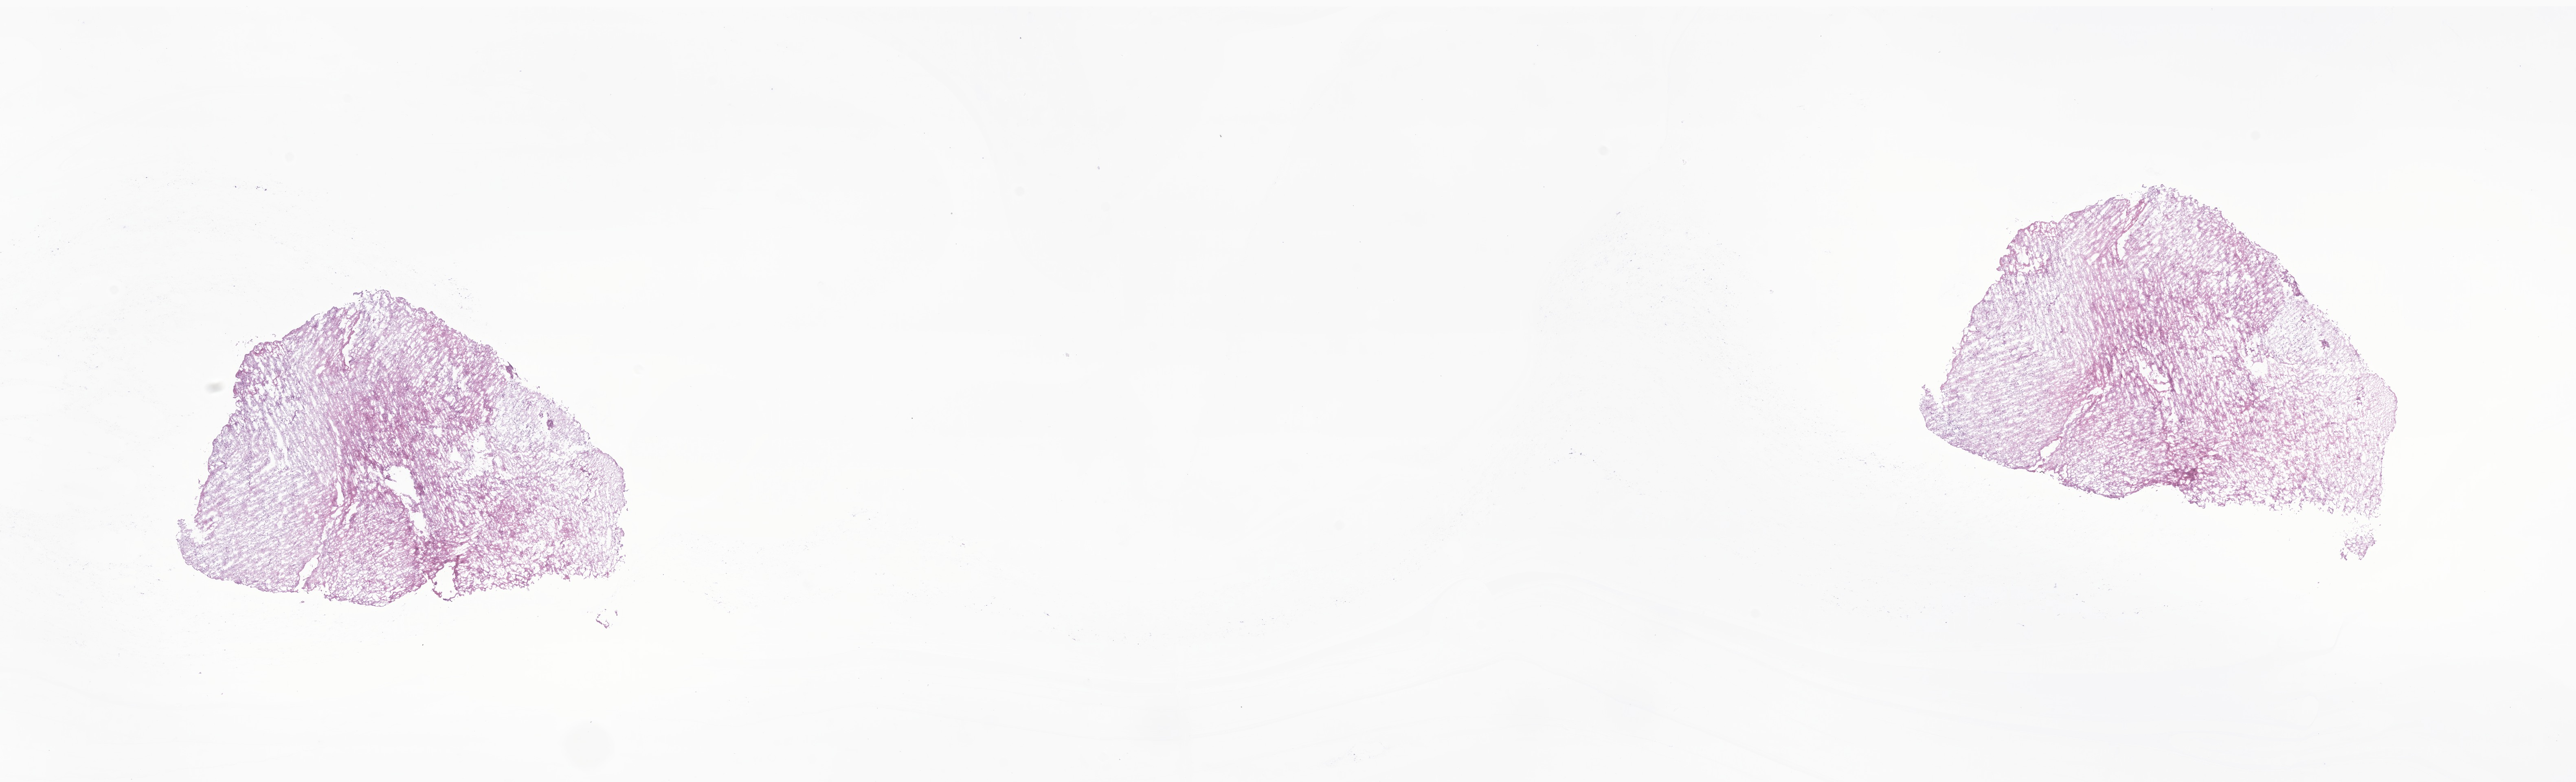
Whole-slide image, haematoxylin and eosin stain of tumor tissue from the brain — low-resolution overview of the scanned area, about 26.7 x 8.1 mm; frozen section (OCT-embedded). Patient: female, age 104 months.
• diagnosis (ICD-O-3 morphology term): Pilocytic astrocytoma